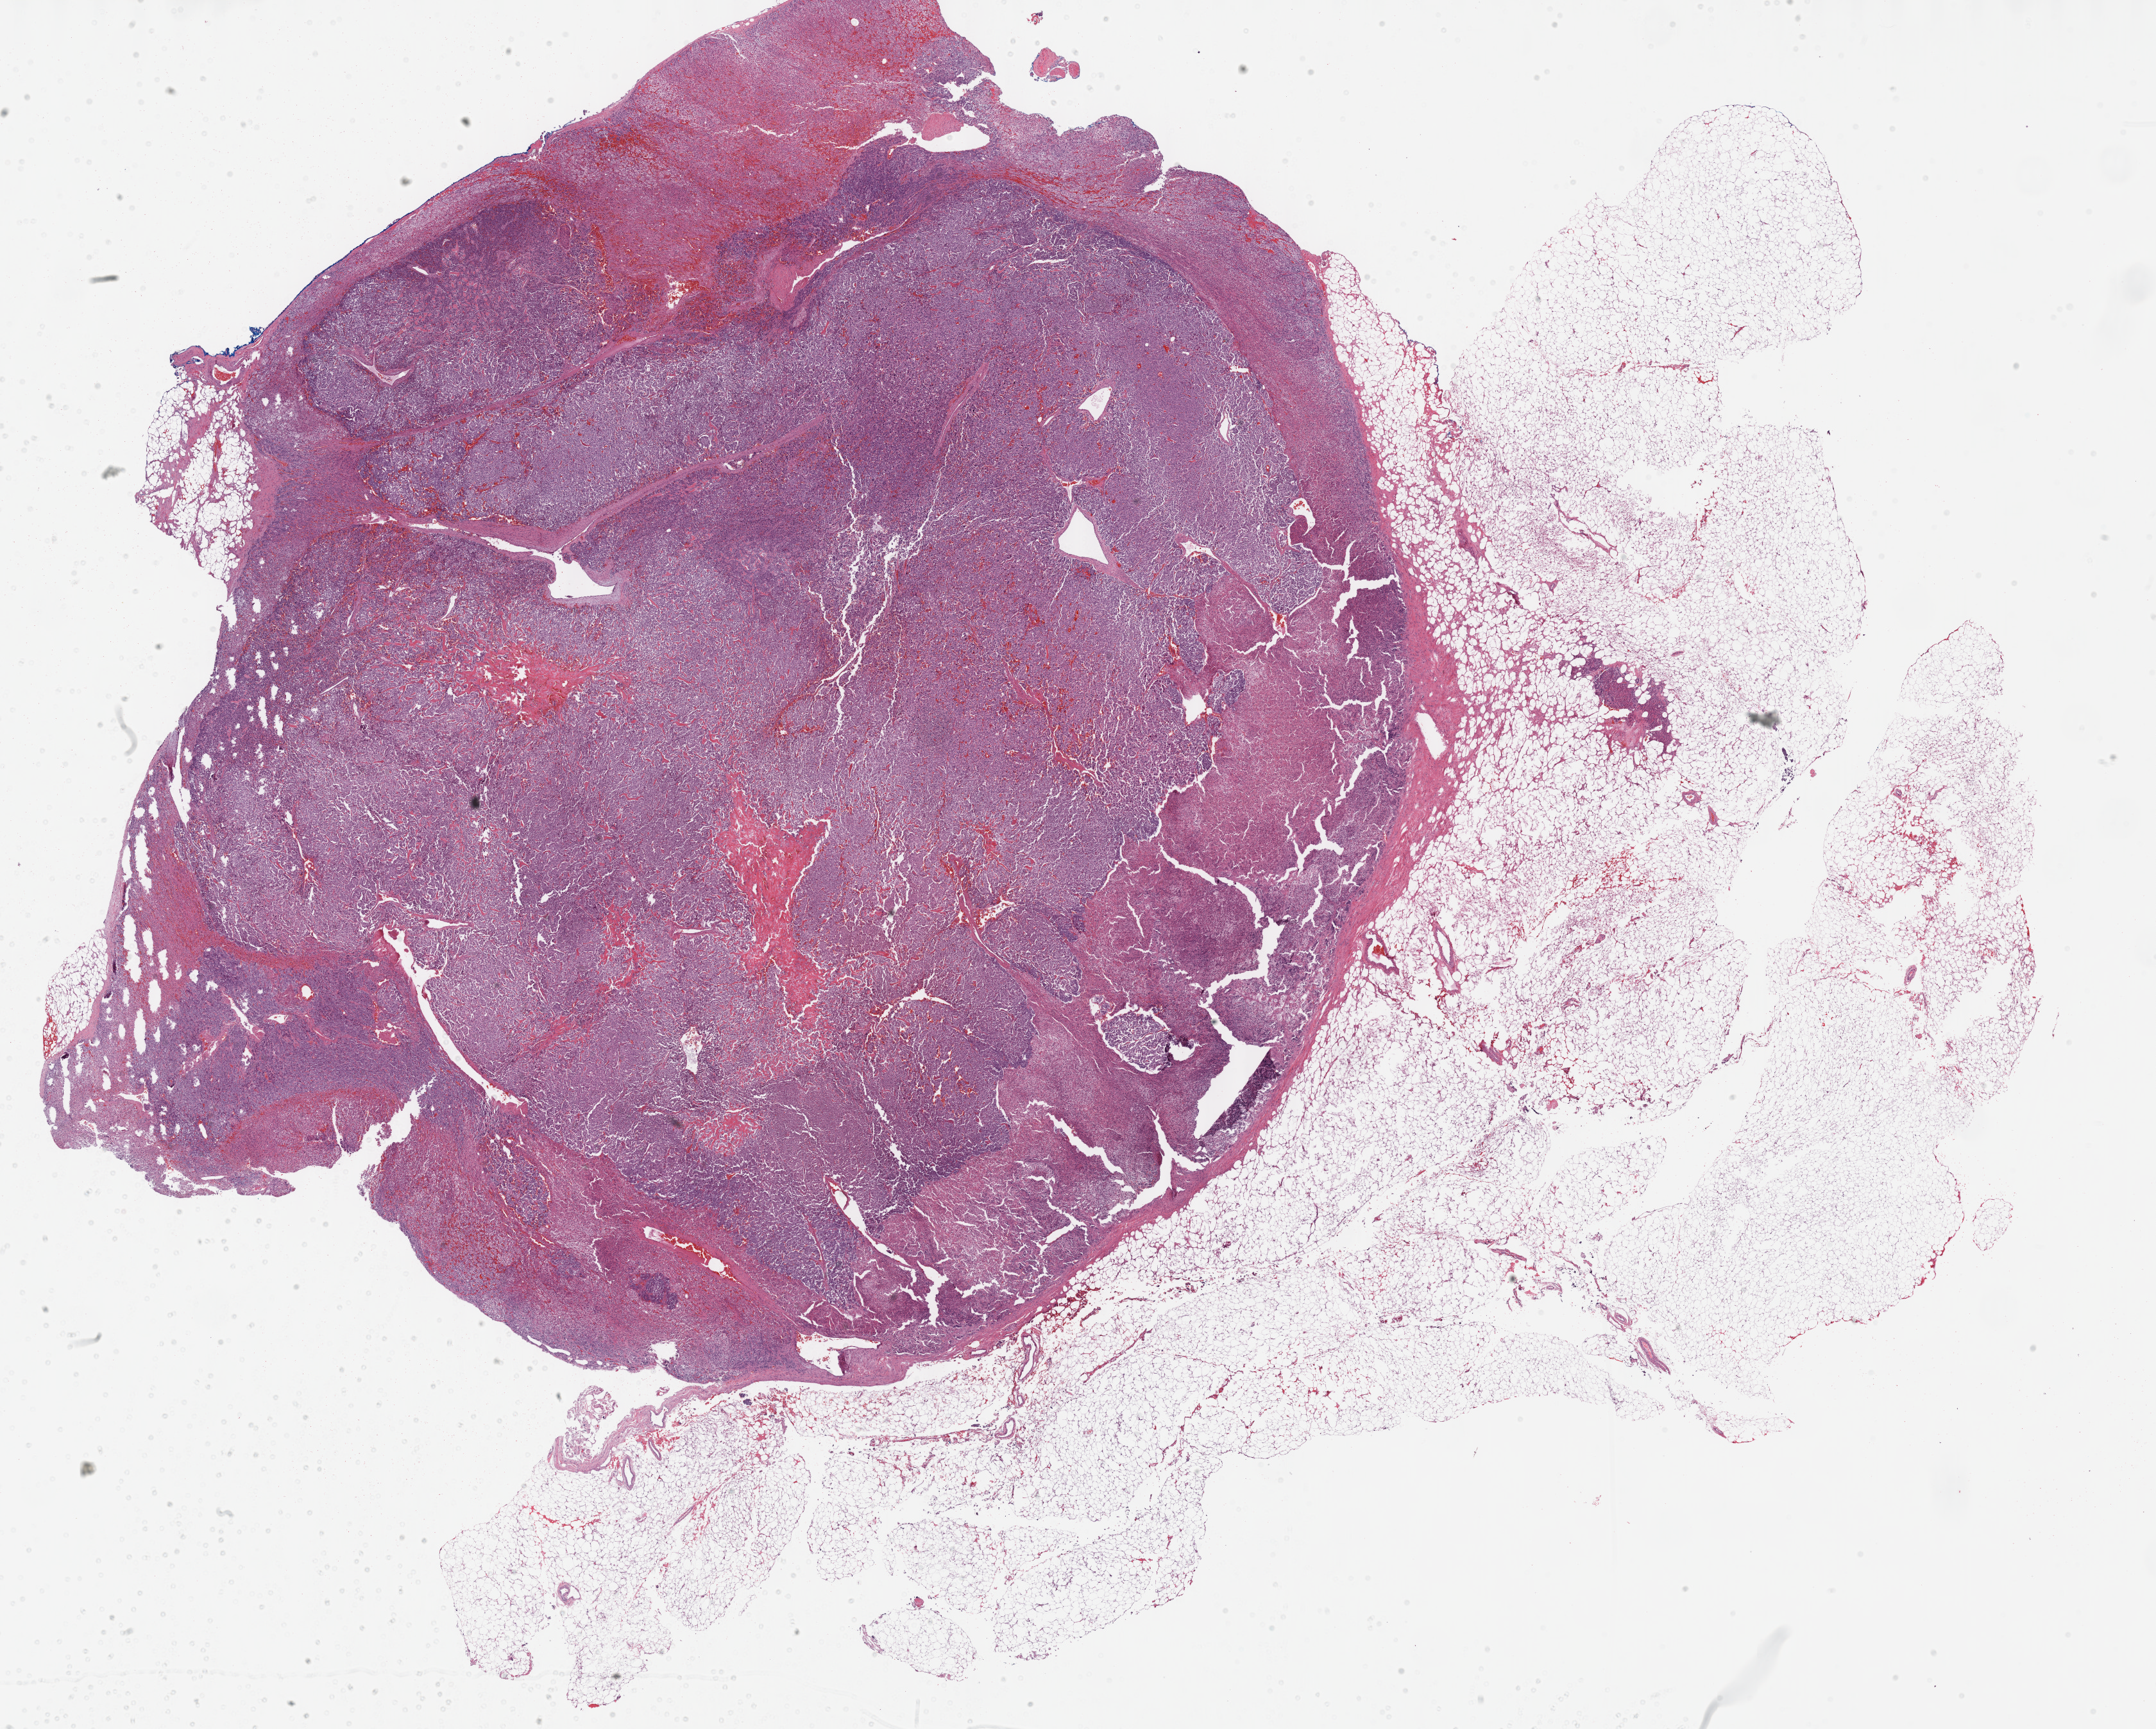
Digitized H&E tissue section (whole slide), low-resolution overview of the scanned area, about 27.2 x 21.8 mm. Formalin-fixed paraffin-embedded (FFPE) diagnostic section. Sample: primary tumour, adrenal gland. Patient: male, age at initial diagnosis 49 years.
• histologic diagnosis: Papillary adenocarcinoma, NOS